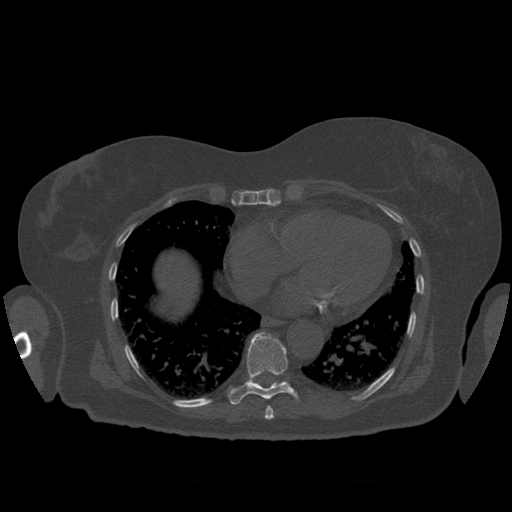
CT including the spine, one axial slice; position 359 of 399 along the scan axis; 120 kVp; bone window (W 1800 / L 400 HU); 1.25 mm slice thickness; 512 × 512 image matrix. Patient age 81 years. From the clinical record (not read from this slice): primary cancer: renal; vertebrae with lytic lesions (as recorded): L1.
Annotated regions visible in this slice (semi-automatic segmentation, software-assisted and operator-edited):
- T10 vertebra: bounding box (x1, y1, x2, y2) in pixels: (277, 381, 289, 385)
- T8 vertebra: (265, 406, 274, 420)
- T9 vertebra: (228, 332, 298, 405)